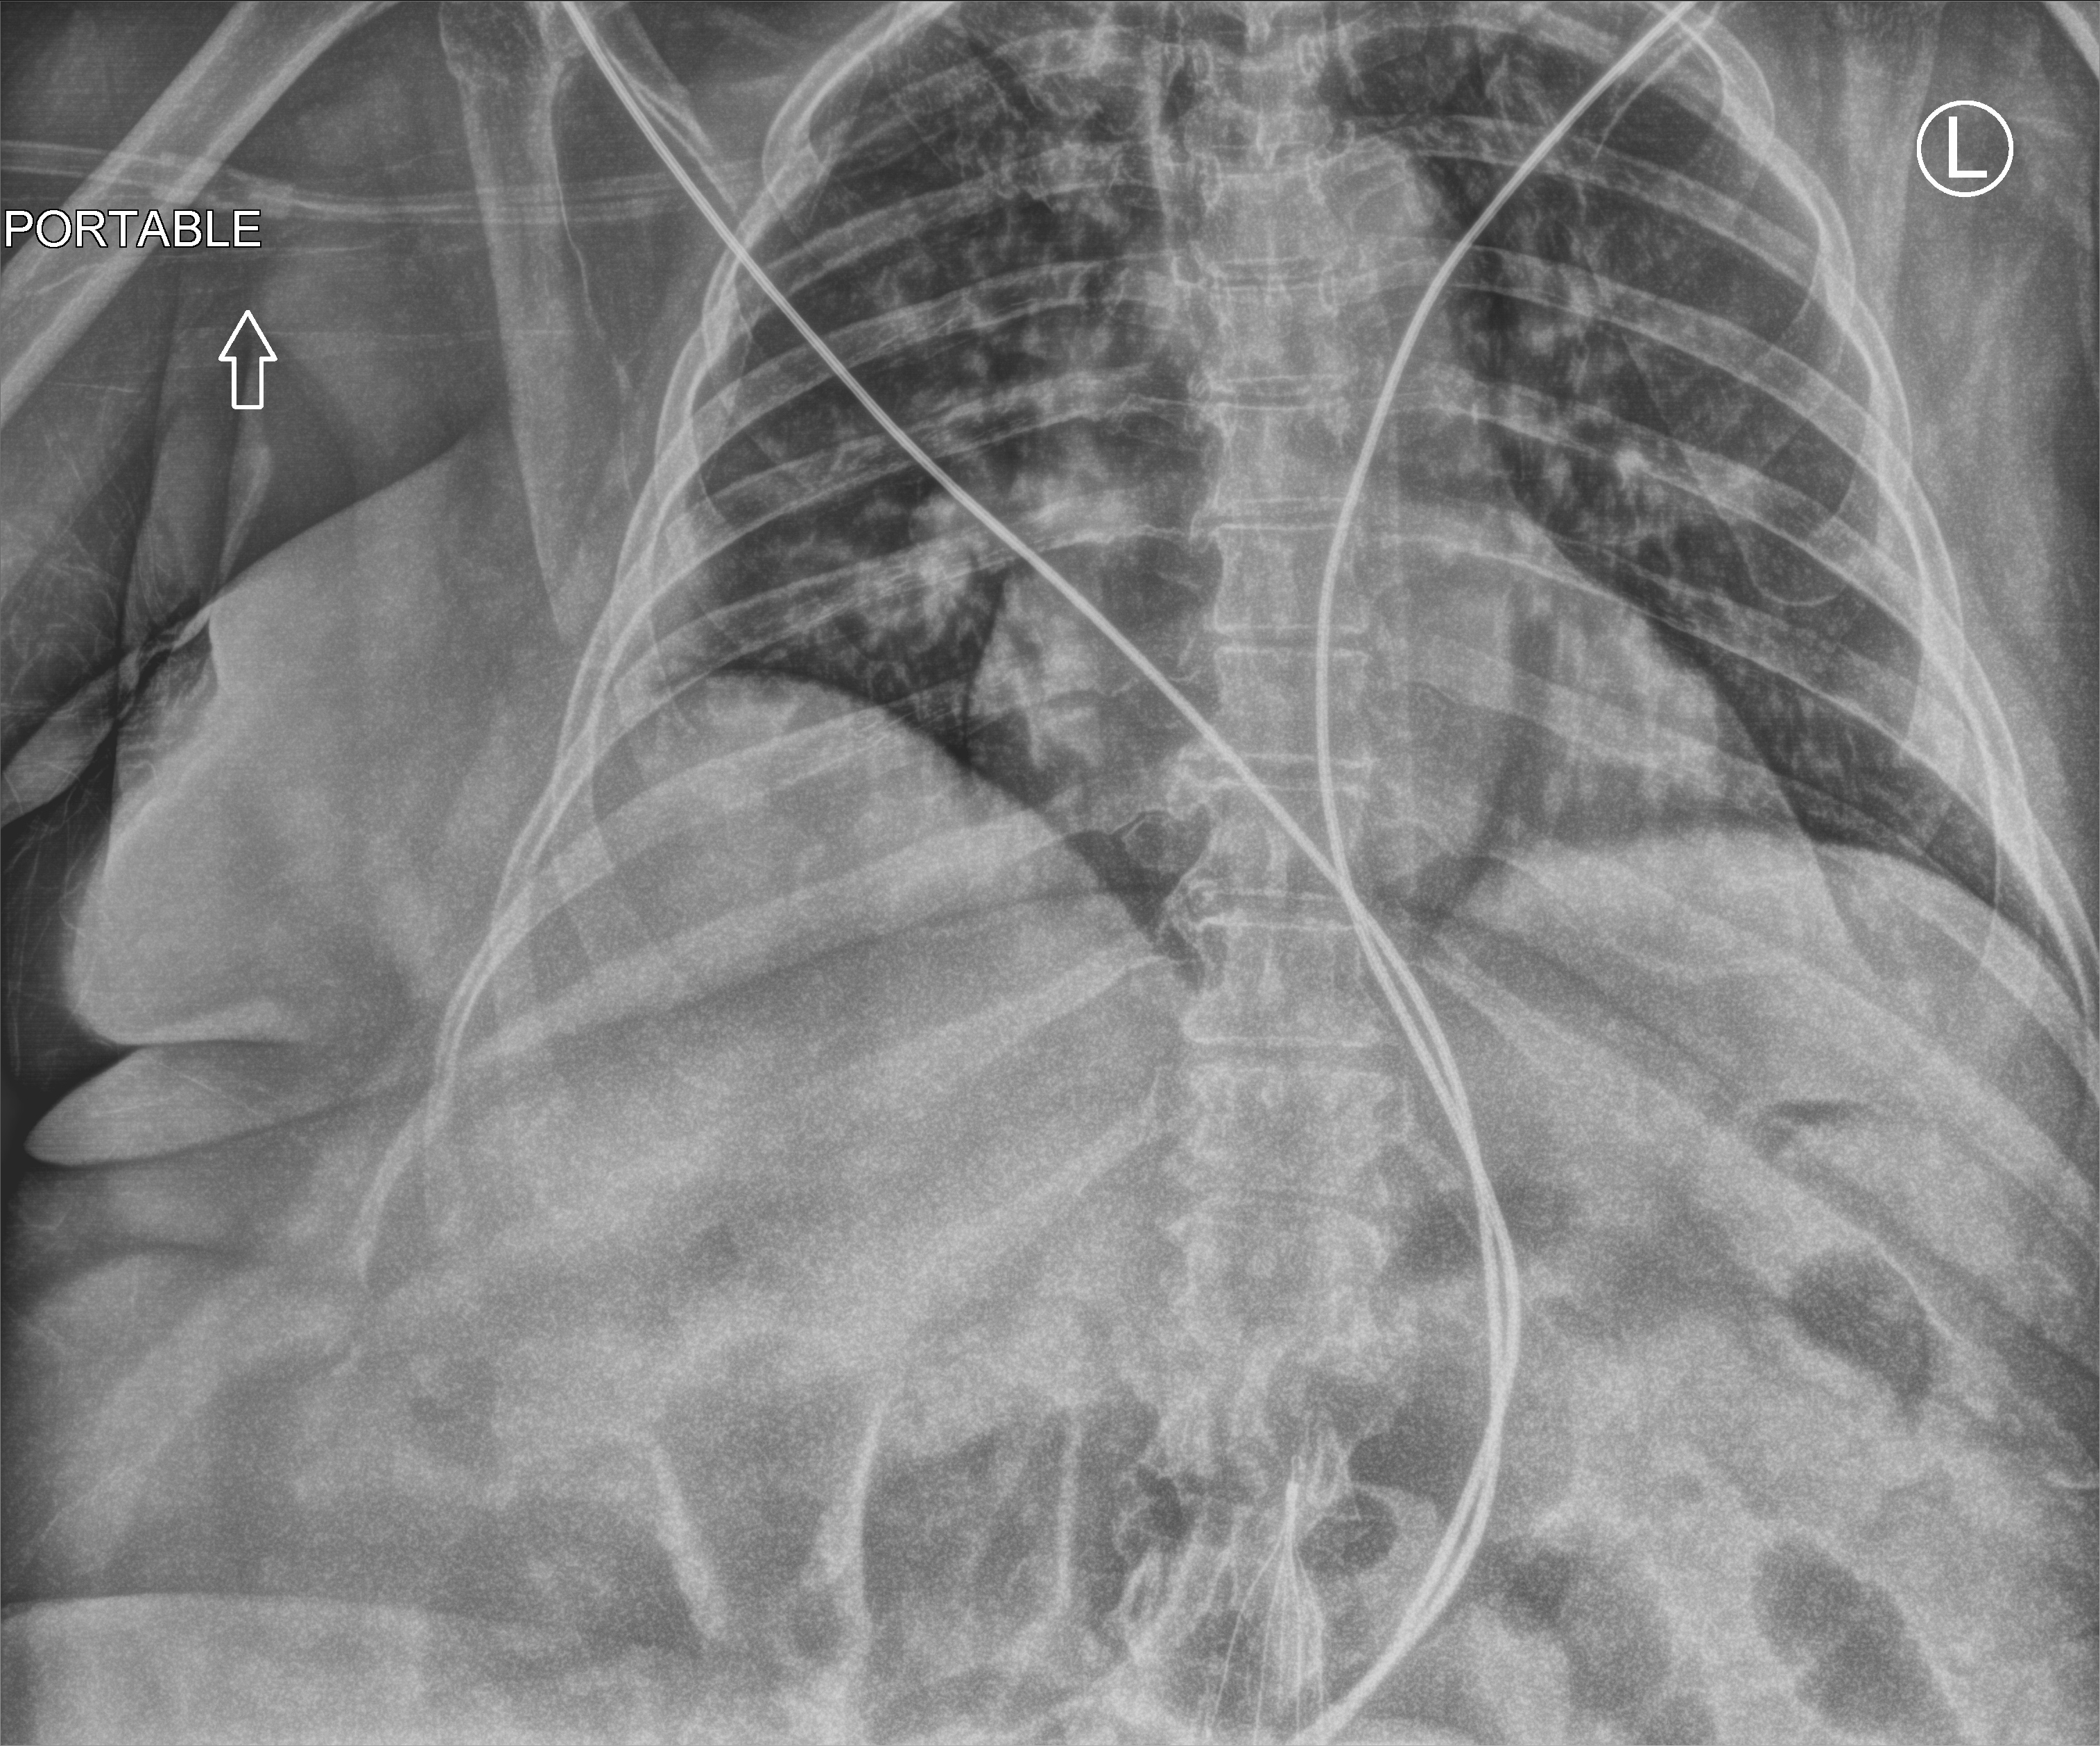
Portable abdomen radiograph. Patient hospitalised with COVID-19; female, aged 60–74 years.
Admission-level facts for this patient (not findings on this image; timing relative to this image not recorded):
- admitted to intensive care during this hospital stay: no
- mechanically ventilated during this hospital stay: no